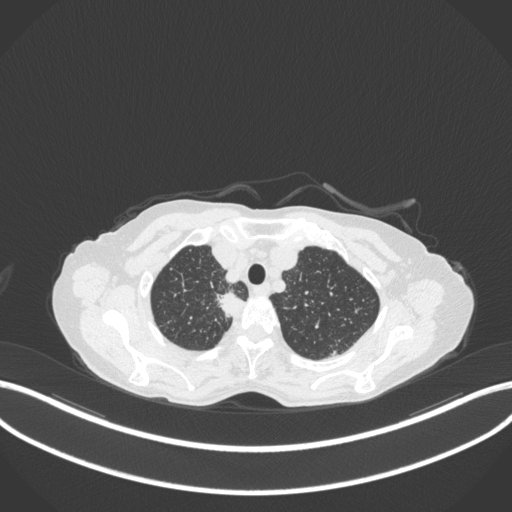
Chest CT, one axial slice; position 317 of 363 along the scan axis; reconstruction kernel B31f; lung window (W 1500 / L -600 HU); 1 mm slice thickness; 512 × 512 image matrix. Female patient, age 75 years. From the clinical record (not read from this slice): clinical TNM (as recorded): T1c N1 M1.
Outlined on this slice (rectangle marked by the reading radiologist):
- lung tumour (recorded histology: adenocarcinoma): box from (x=212, y=285) to (x=248, y=322) px